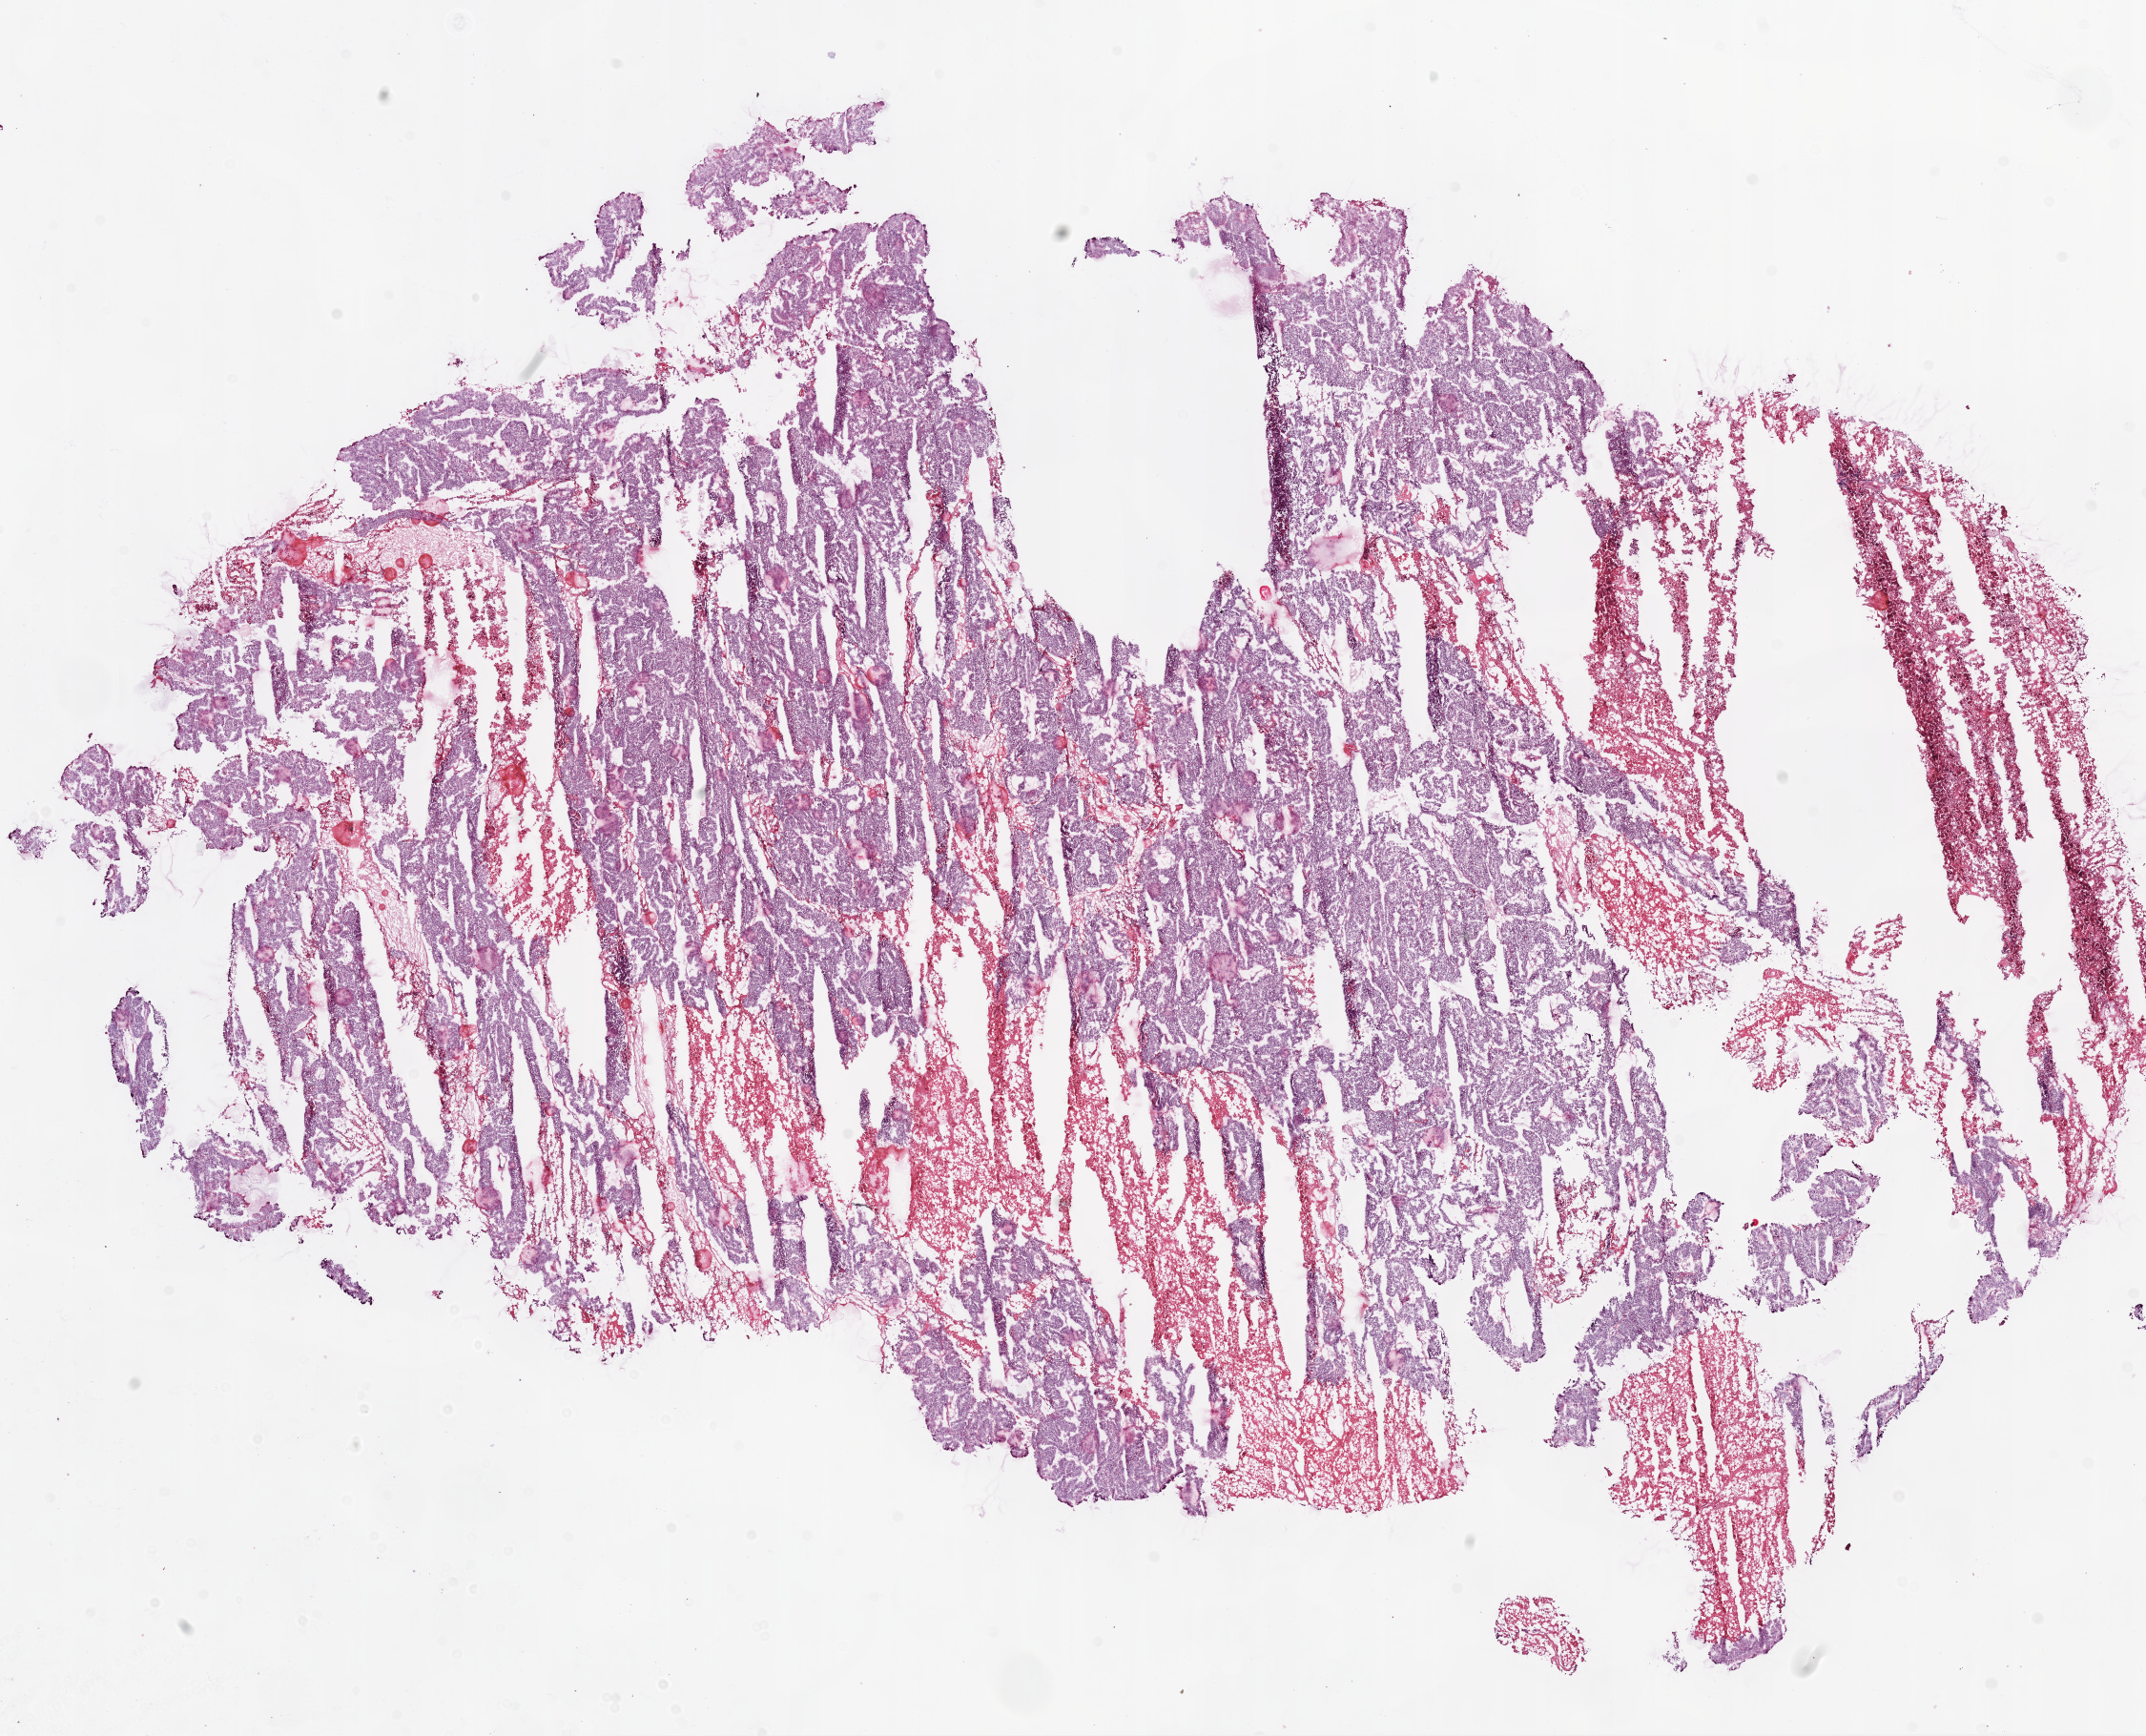
H&E-stained whole-slide image — shown as a low-resolution overview of the whole scanned area (about 18.1 x 14.6 mm); frozen section; recurrent tumour sample from the ovary. Patient: female, age at initial diagnosis 58 years. Composition of this section per pathologist review: tumour cells 60%, tumour nuclei 90%, normal cells 0%, stromal cells 20%, necrosis 20%.
This section: recurrent tumour. Patient diagnosis: Serous cystadenocarcinoma, NOS.